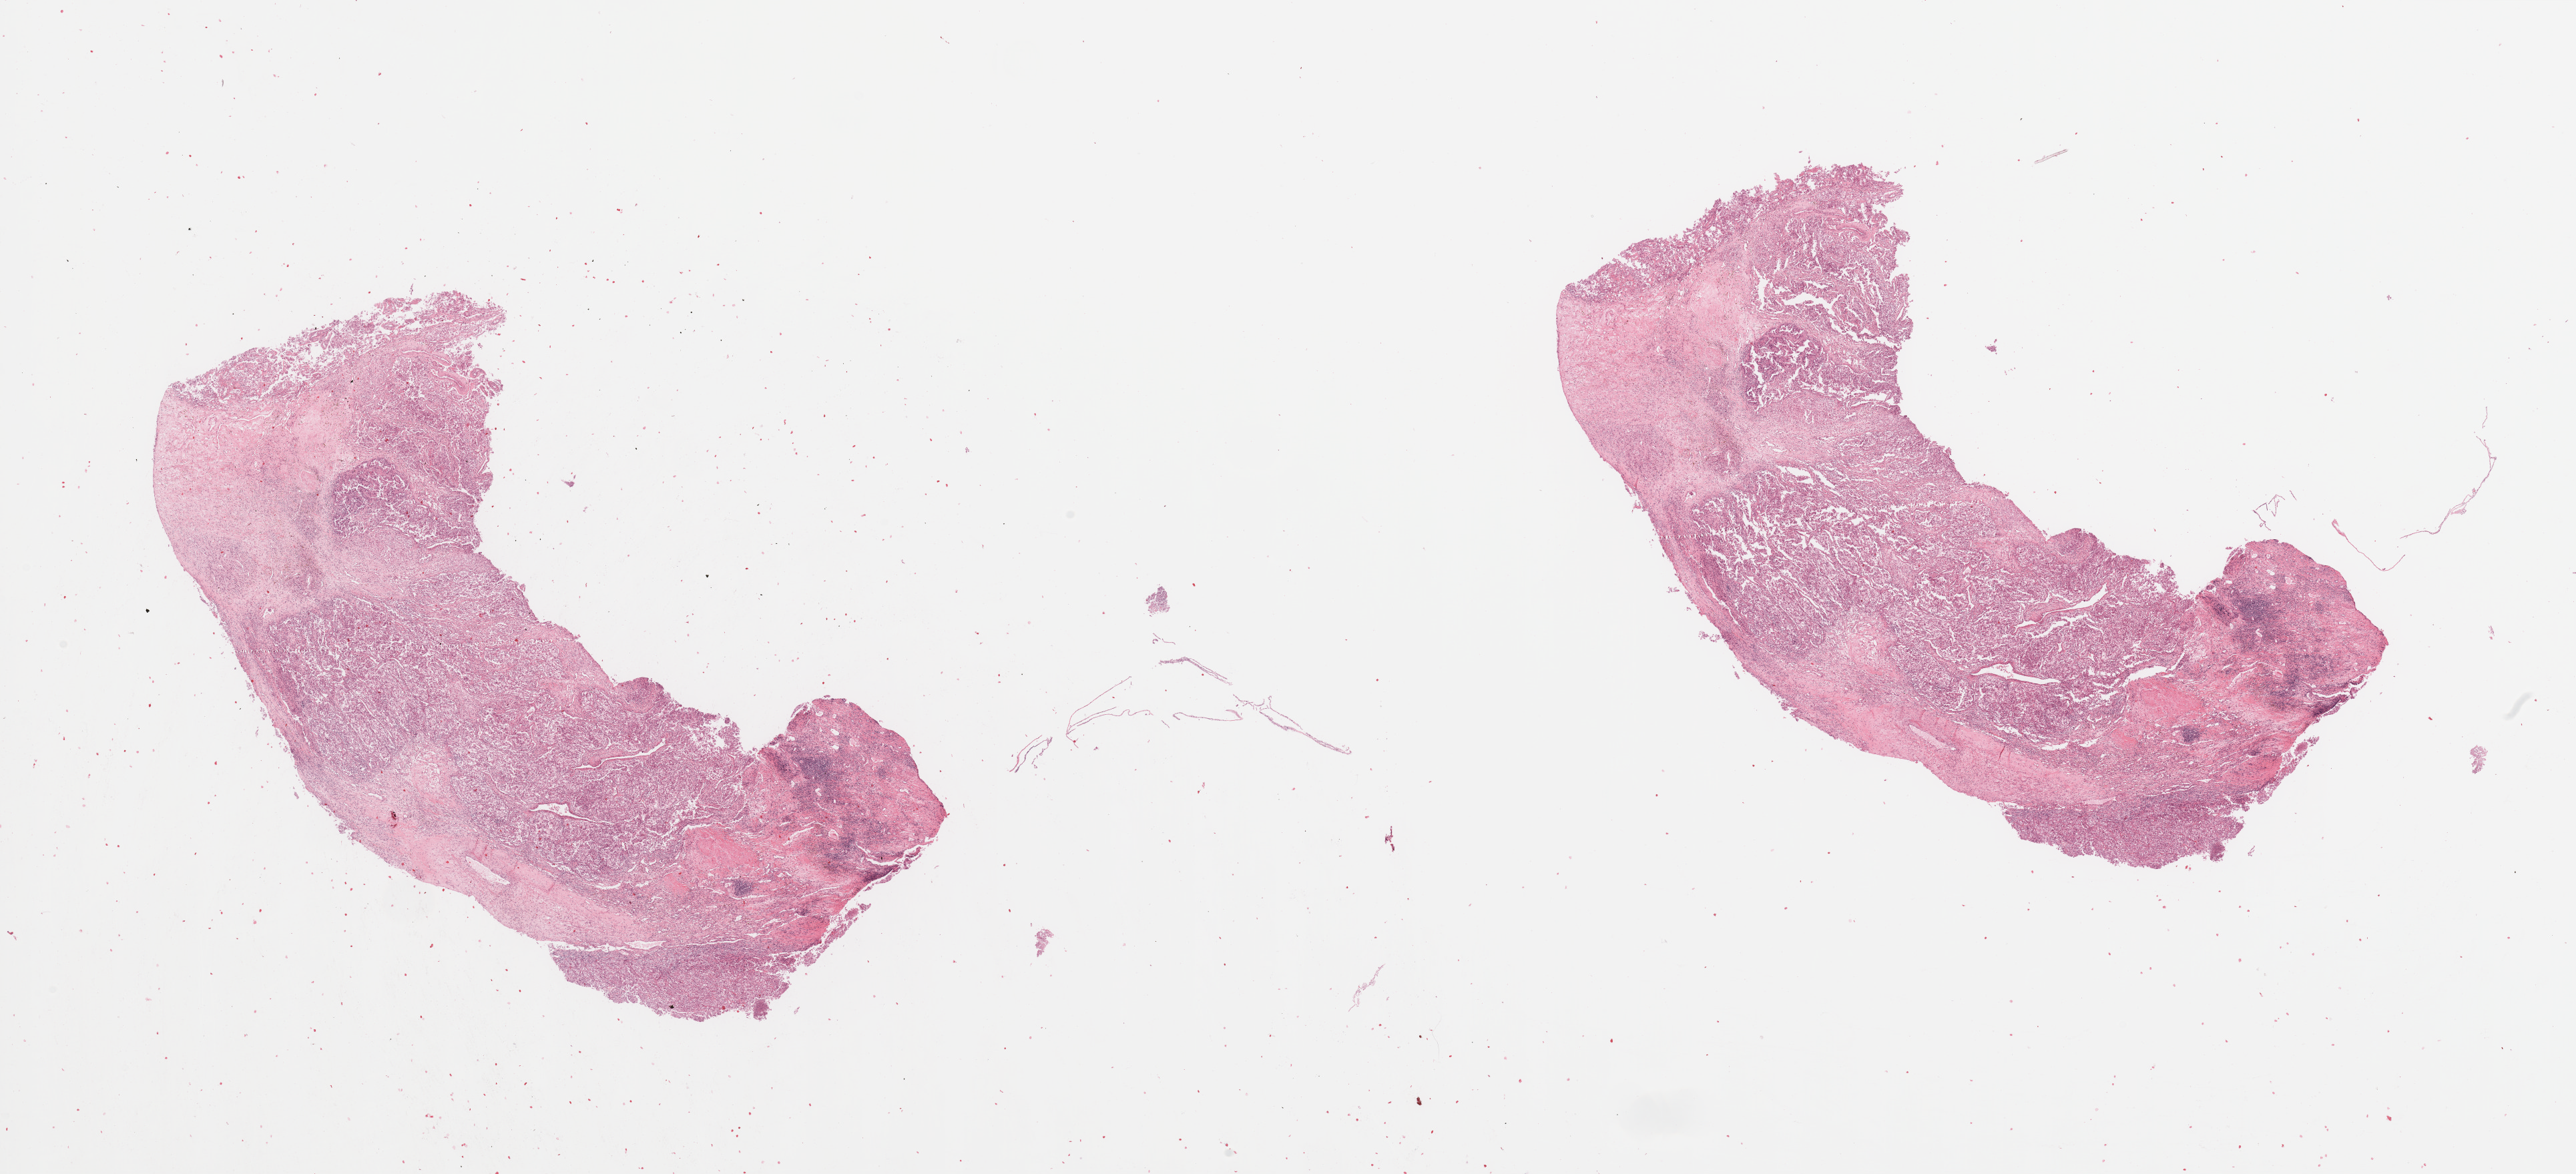
Whole-slide histology image, Hematoxylin and eosin (H&E) stained, low-resolution overview of the scanned area, about 30.5 x 13.9 mm. Tumour tissue sample, sampled site: kidney. Patient: male, age 57 years. Histologic grade: G4 (undifferentiated). Pathologist review of this section (percent, as recorded): tumour nuclei 80%, necrosis 5%.
- diagnosis: Renal cell carcinoma, NOS
- AJCC pathologic stage: III